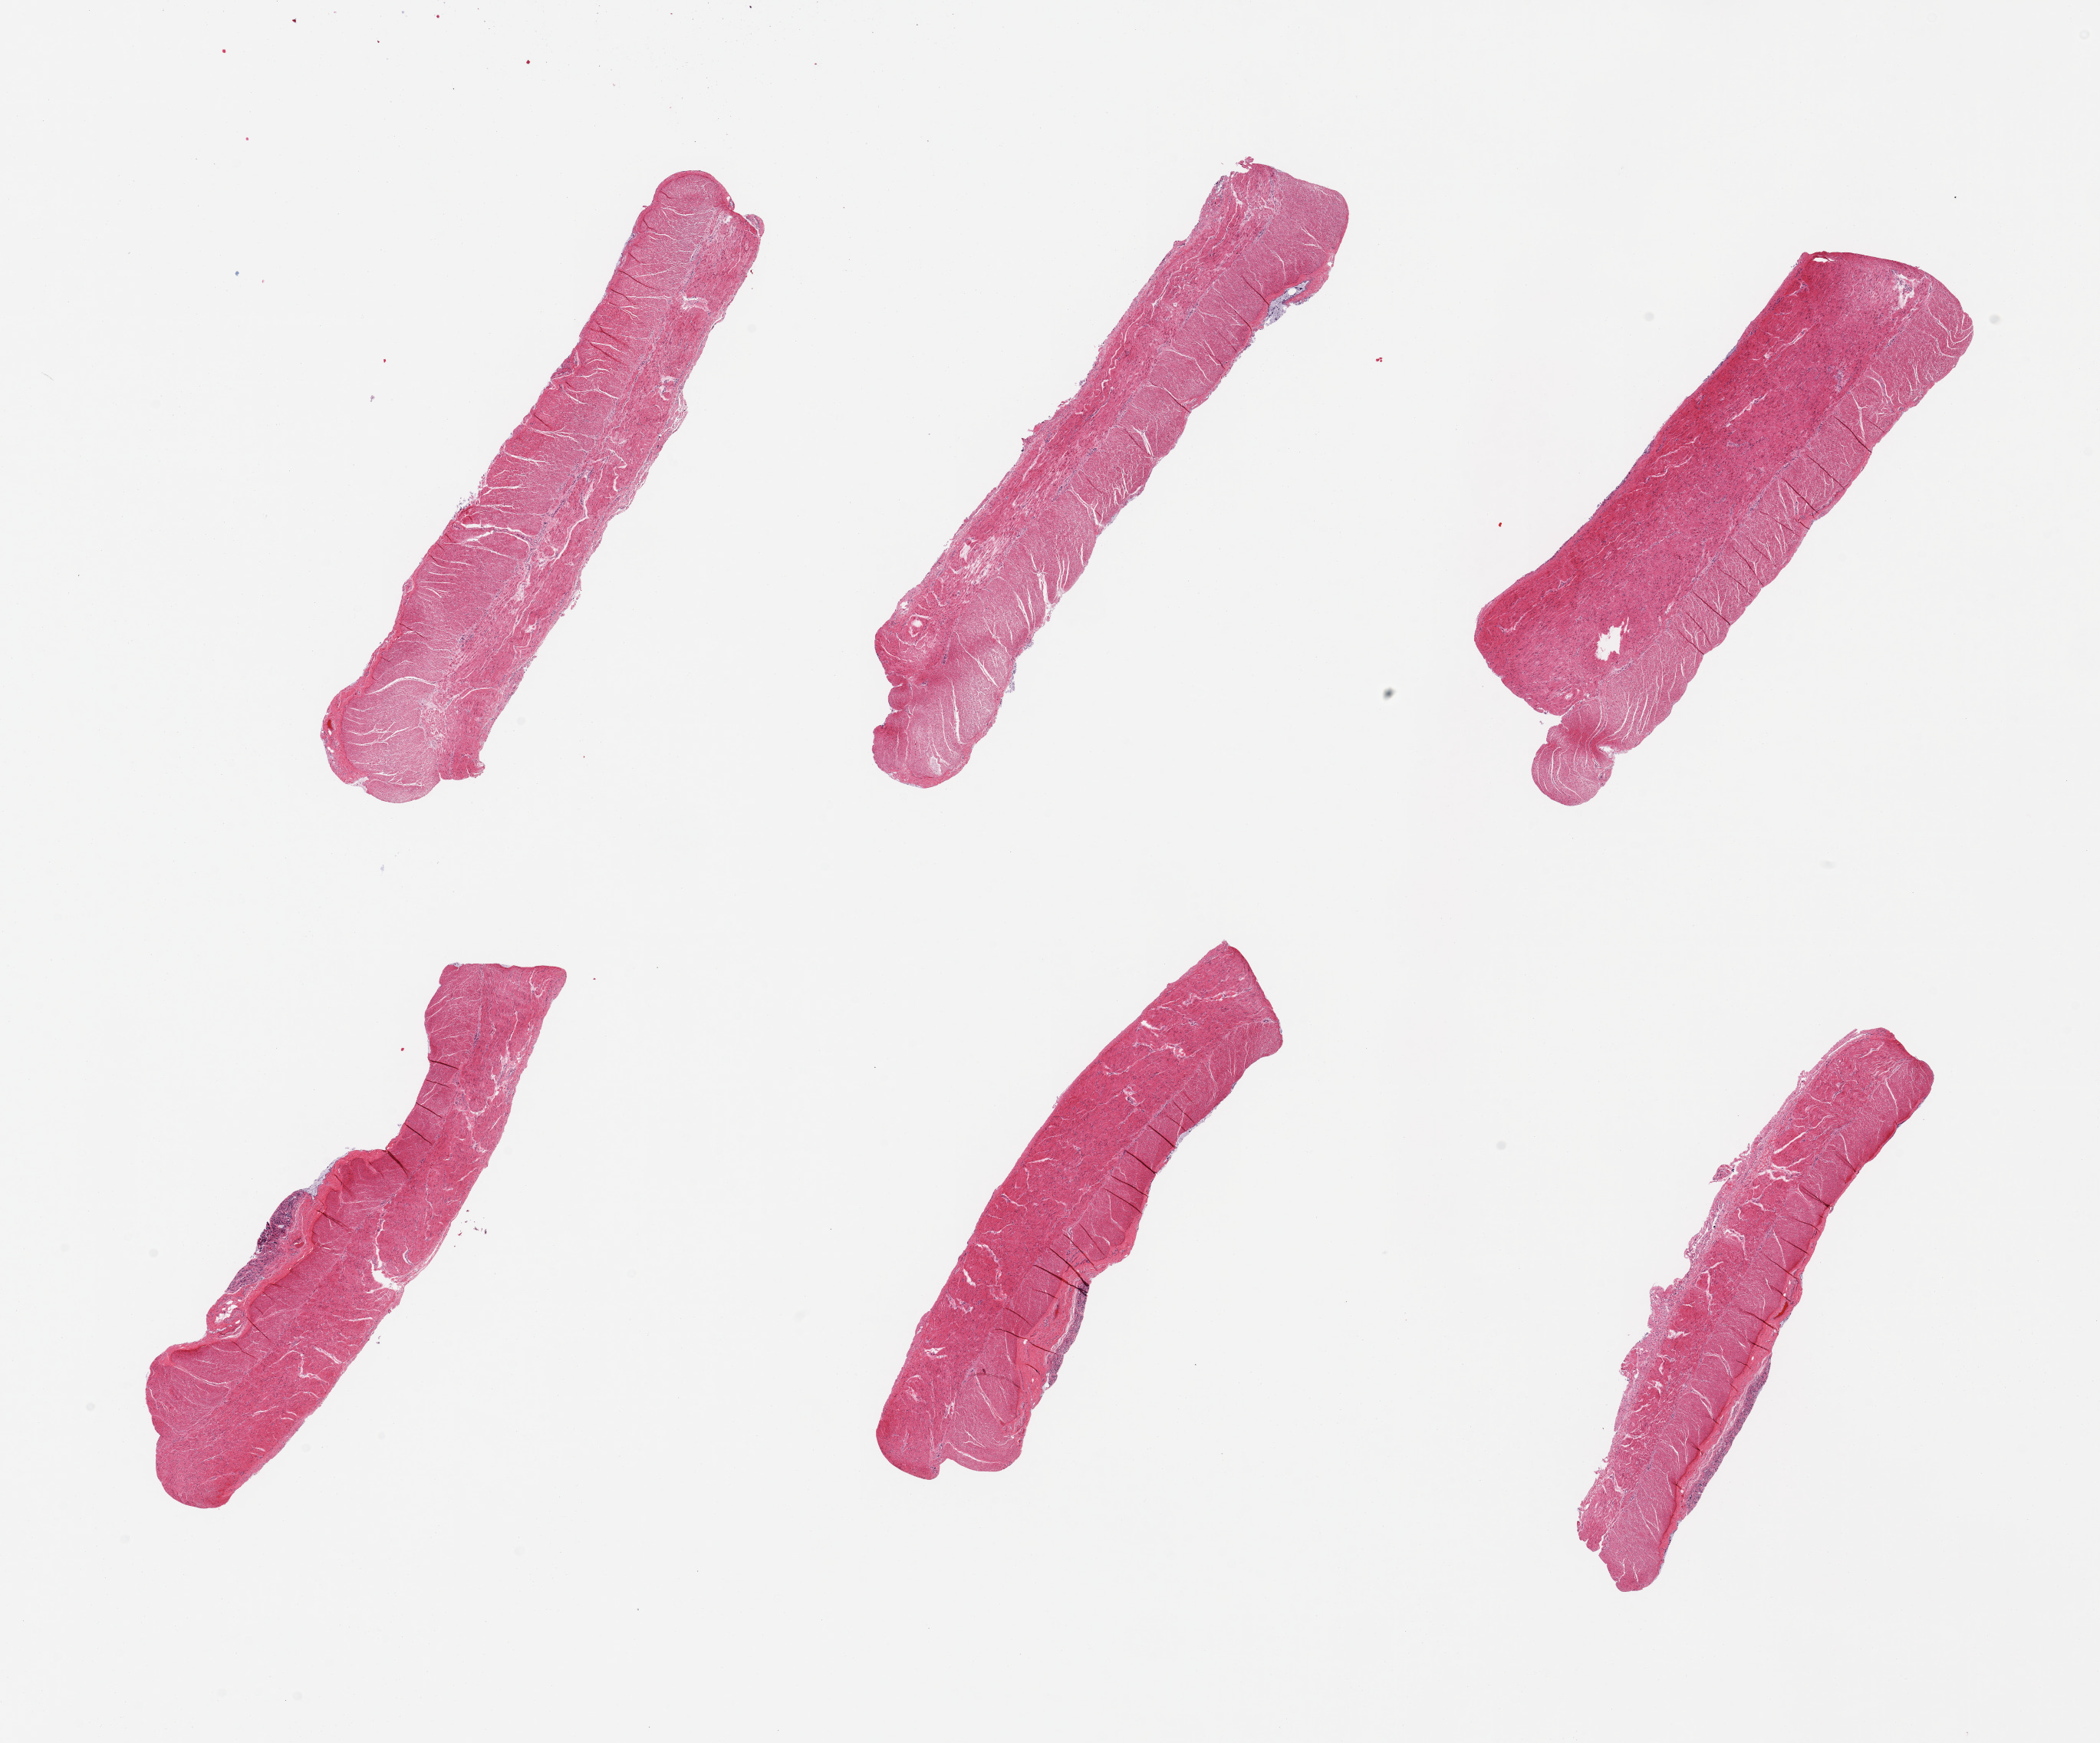
Whole-slide image, hematoxylin and eosin (H&E) stain, brightfield — shown as a low-resolution overview of the whole scanned area (about 21.7 x 18.0 mm). PAXgene-fixed, paraffin-embedded tissue. Target tissue: sigmoid colon. Tissue donor sample. Female donor.
Review note (as recorded): 6 pieces; well dissected muscle.